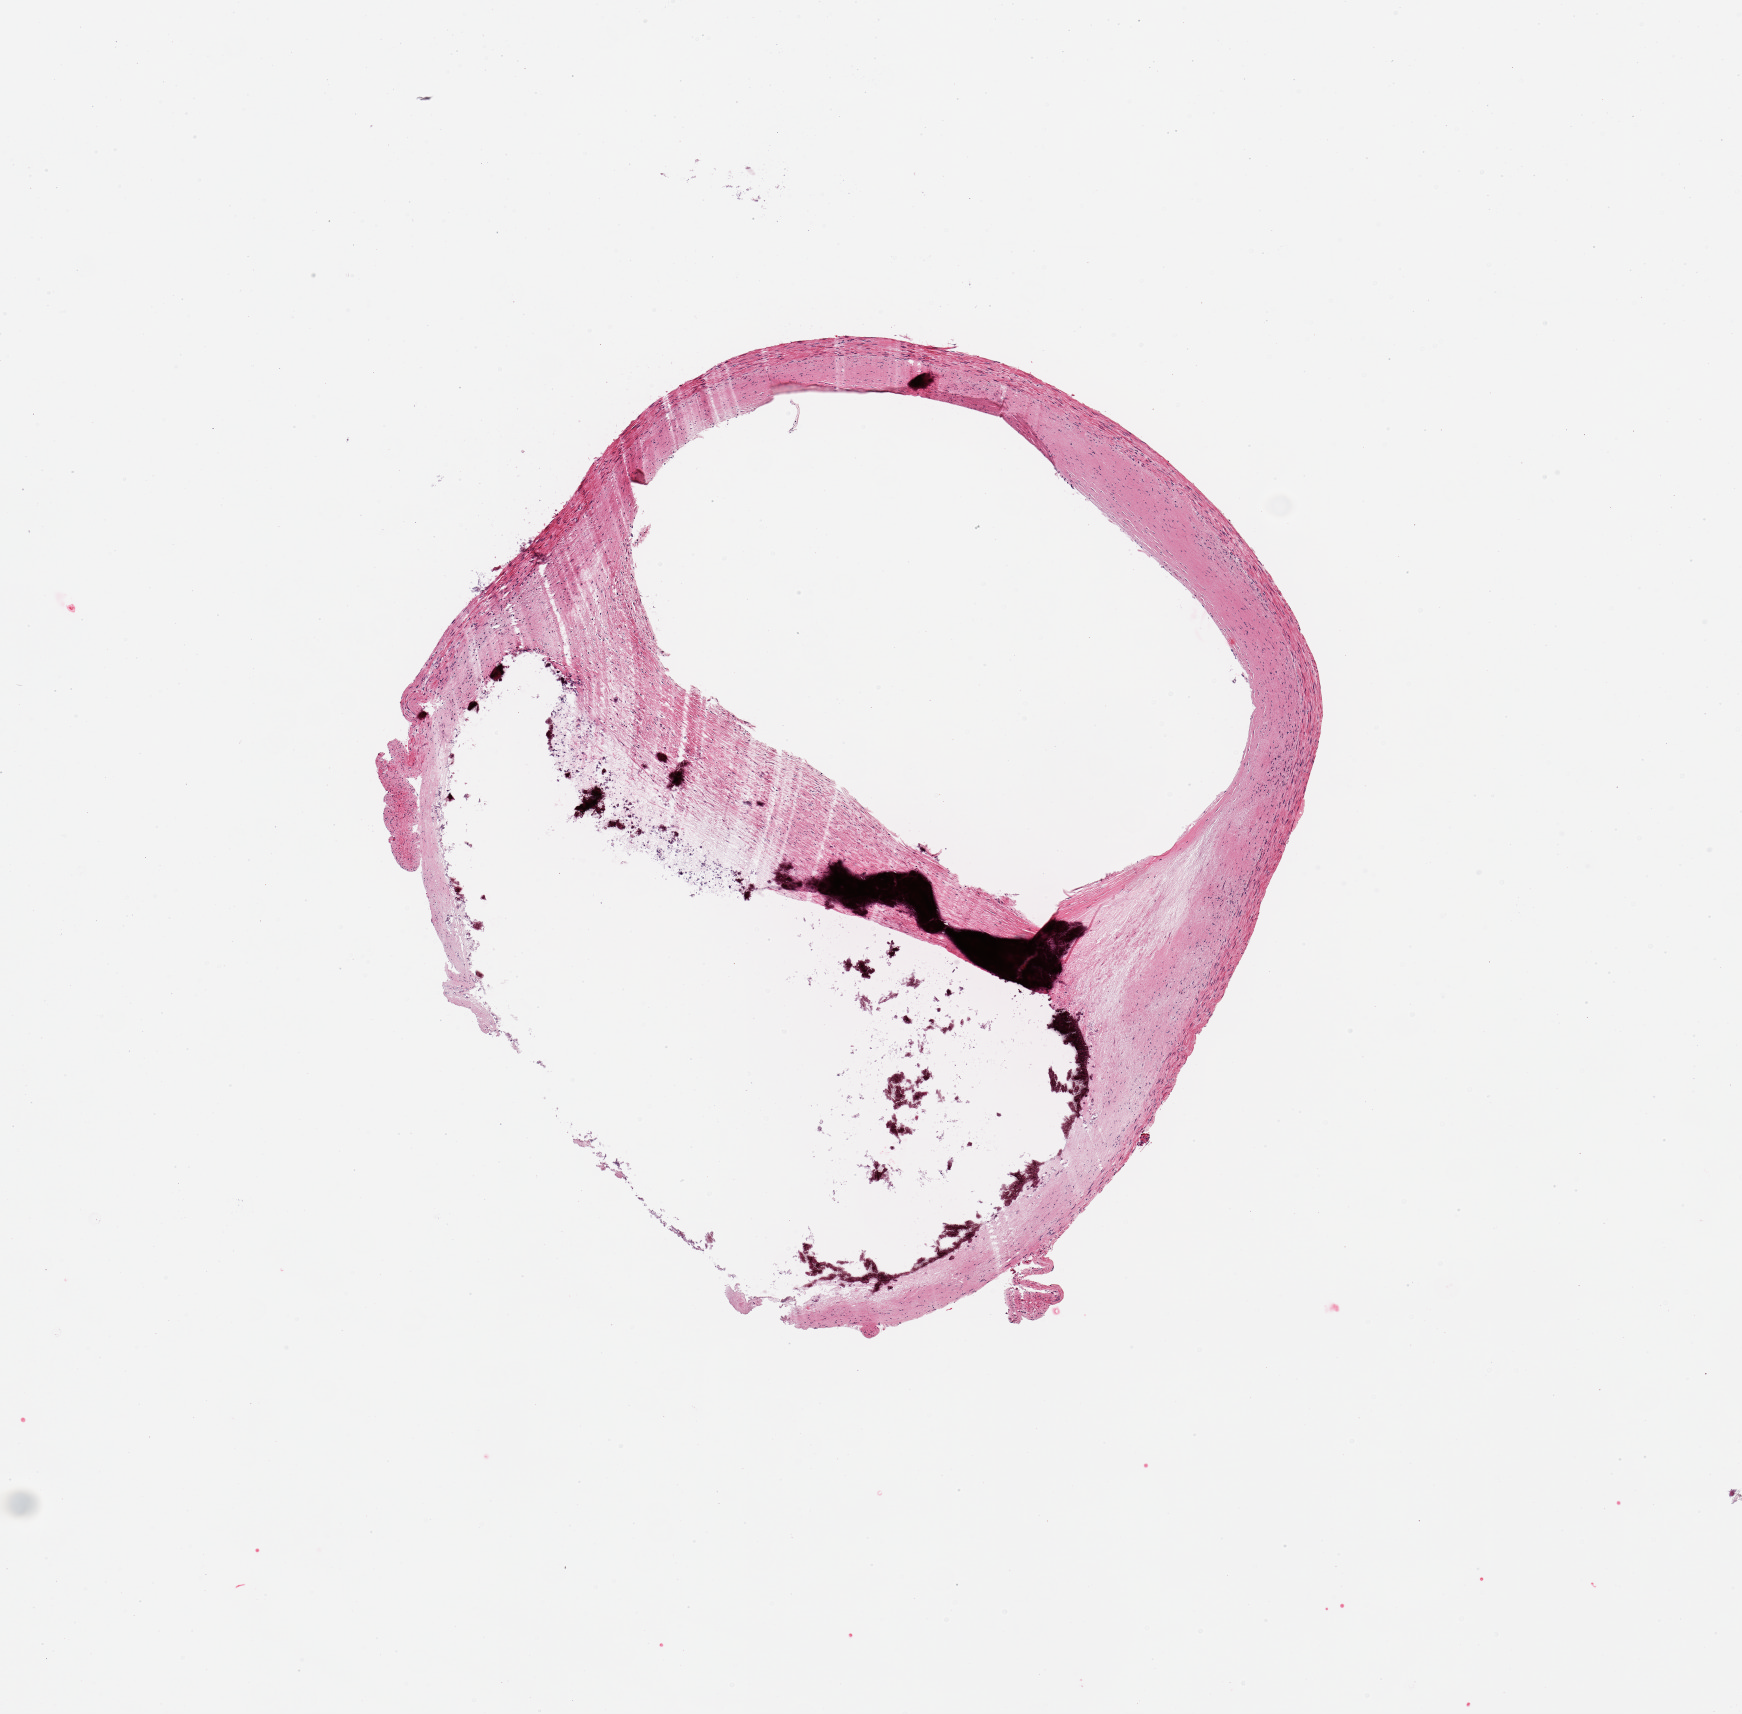
Digitized H&E-stained section, brightfield — whole scanned area (about 6.9 x 6.8 mm, acquisition: 20x scan) shown as a low-resolution overview, PAXgene-fixed, paraffin-embedded tissue, target tissue: coronary artery, donor tissue sample. Donor: male.
Pathologist's review note for this sample: 1 piece; ~60% occlusive calcifying atherosis.